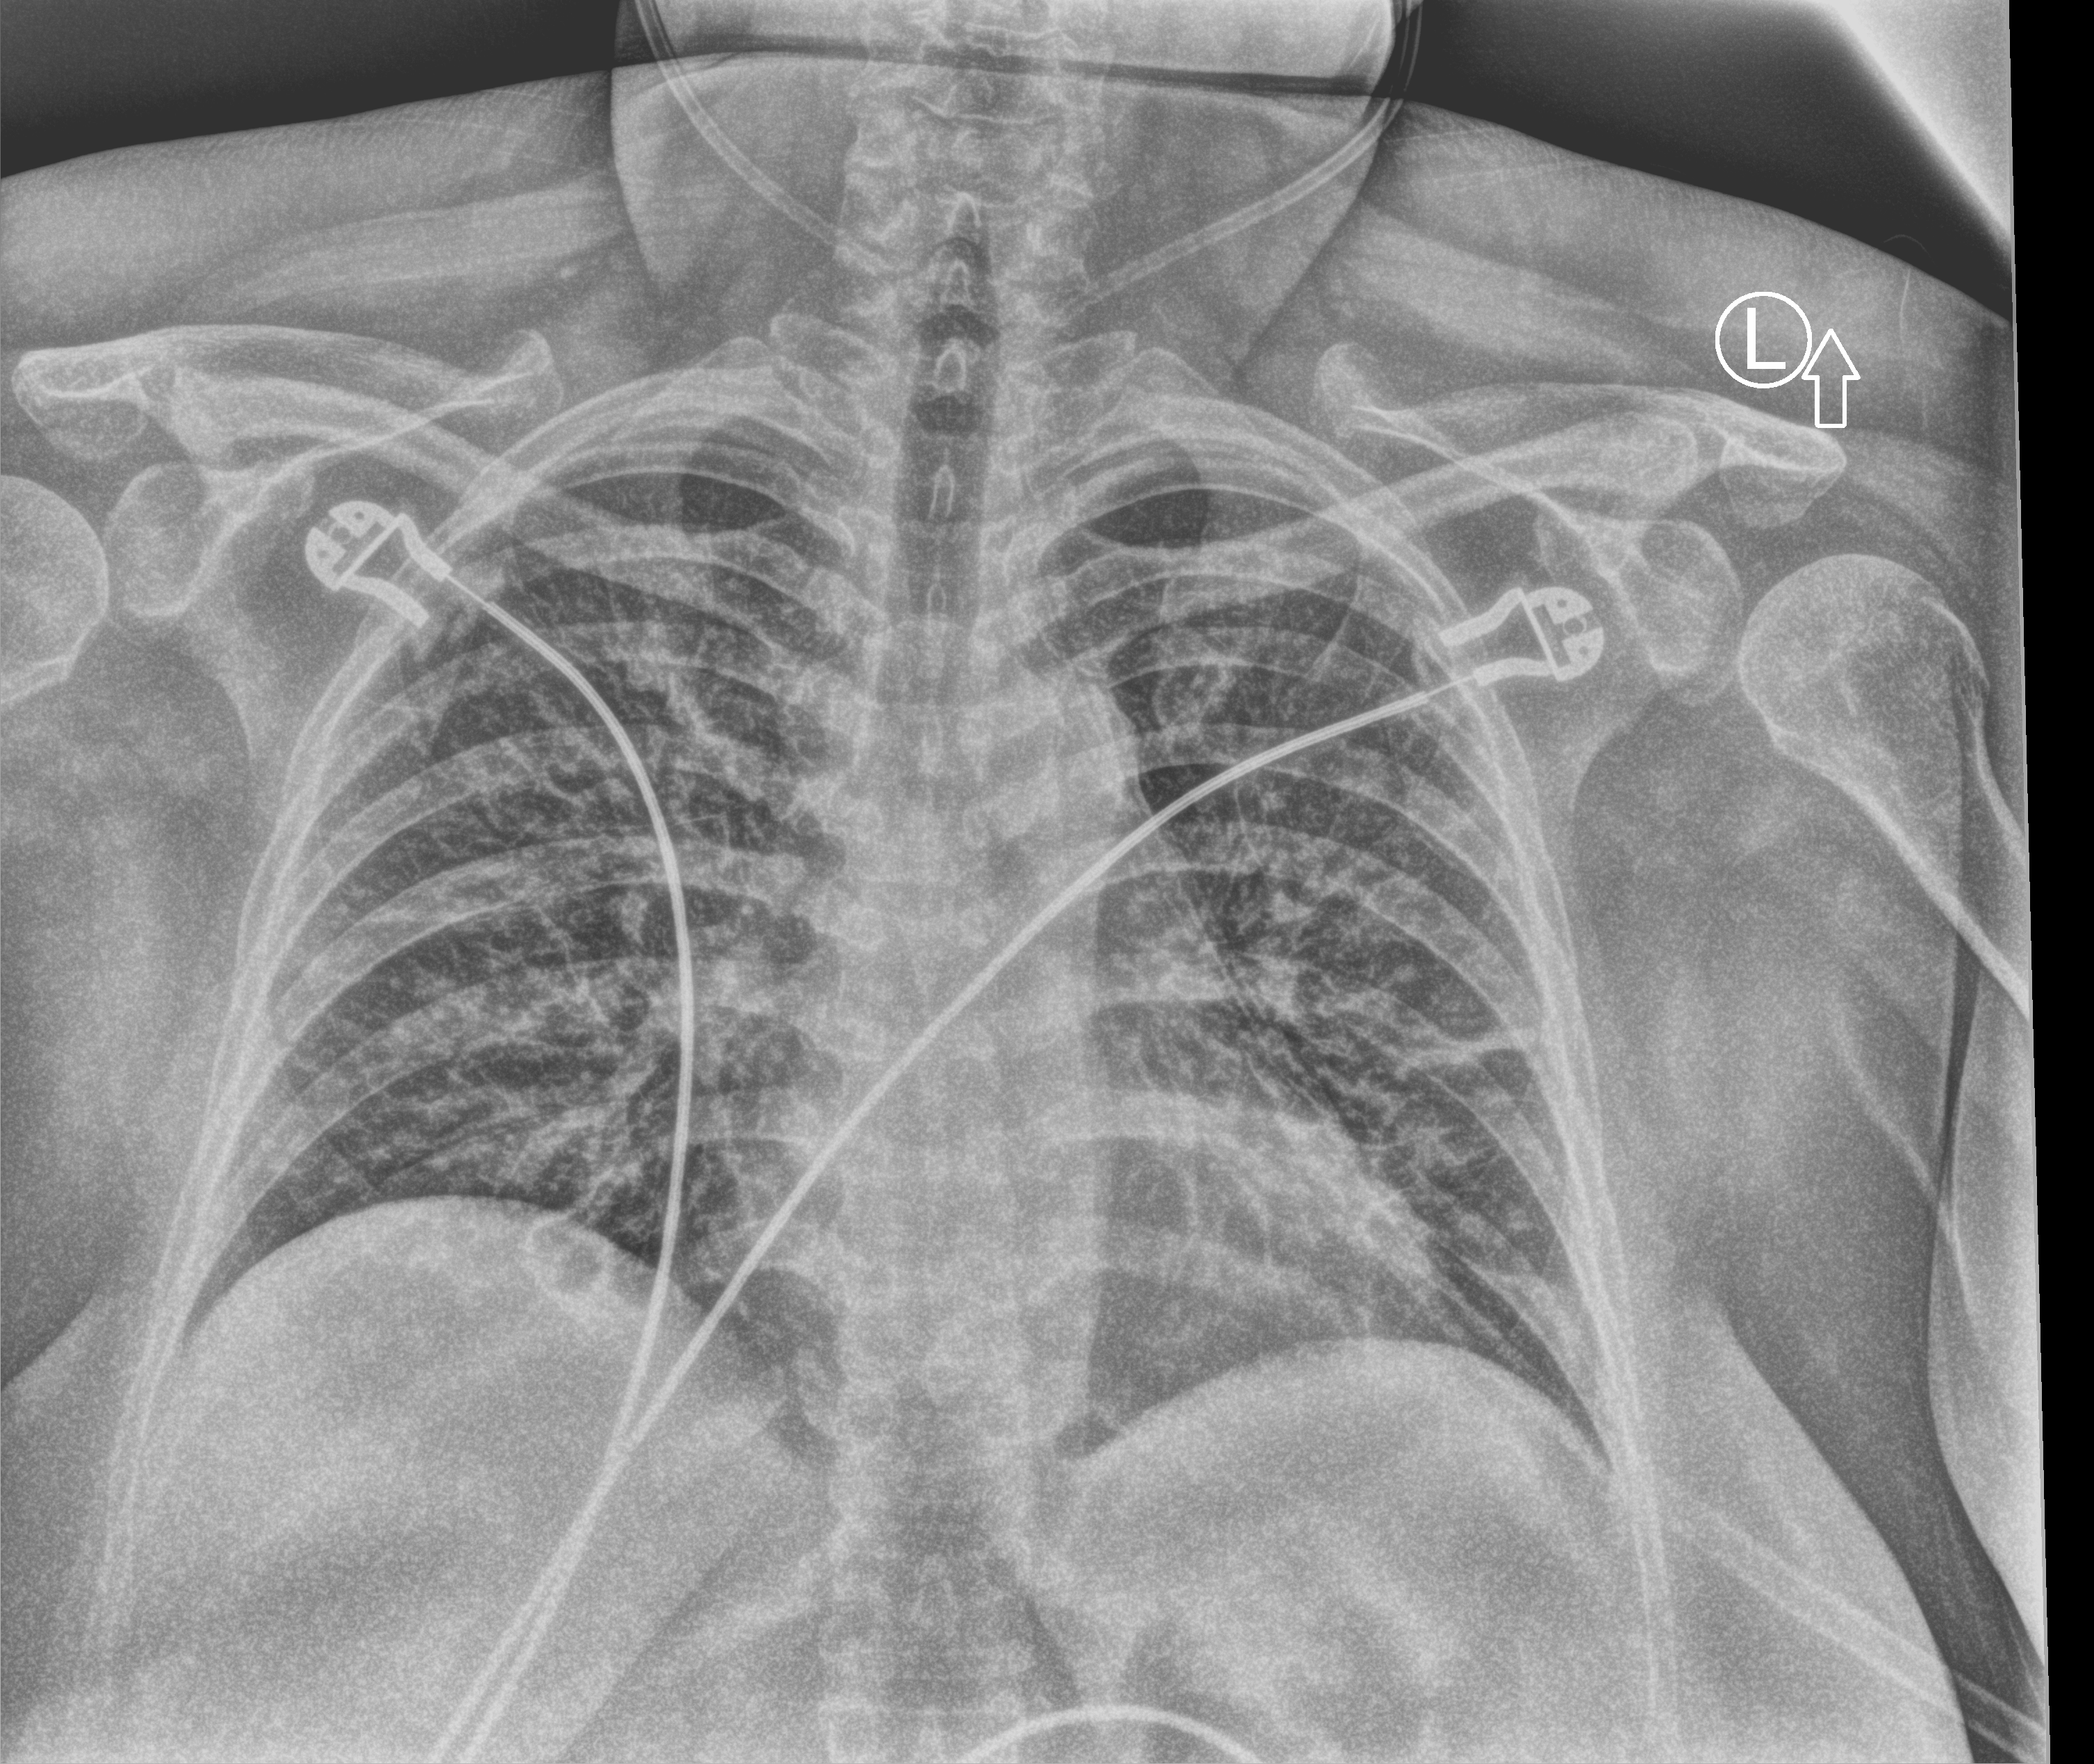
Portable chest radiograph, anteroposterior (AP) projection. Patient hospitalised with COVID-19; female, aged 18–59 years.
Hospital-stay facts (about this admission, not read from this image; timing relative to this image not recorded): admitted to intensive care during this hospital stay: no; mechanically ventilated during this hospital stay: no.